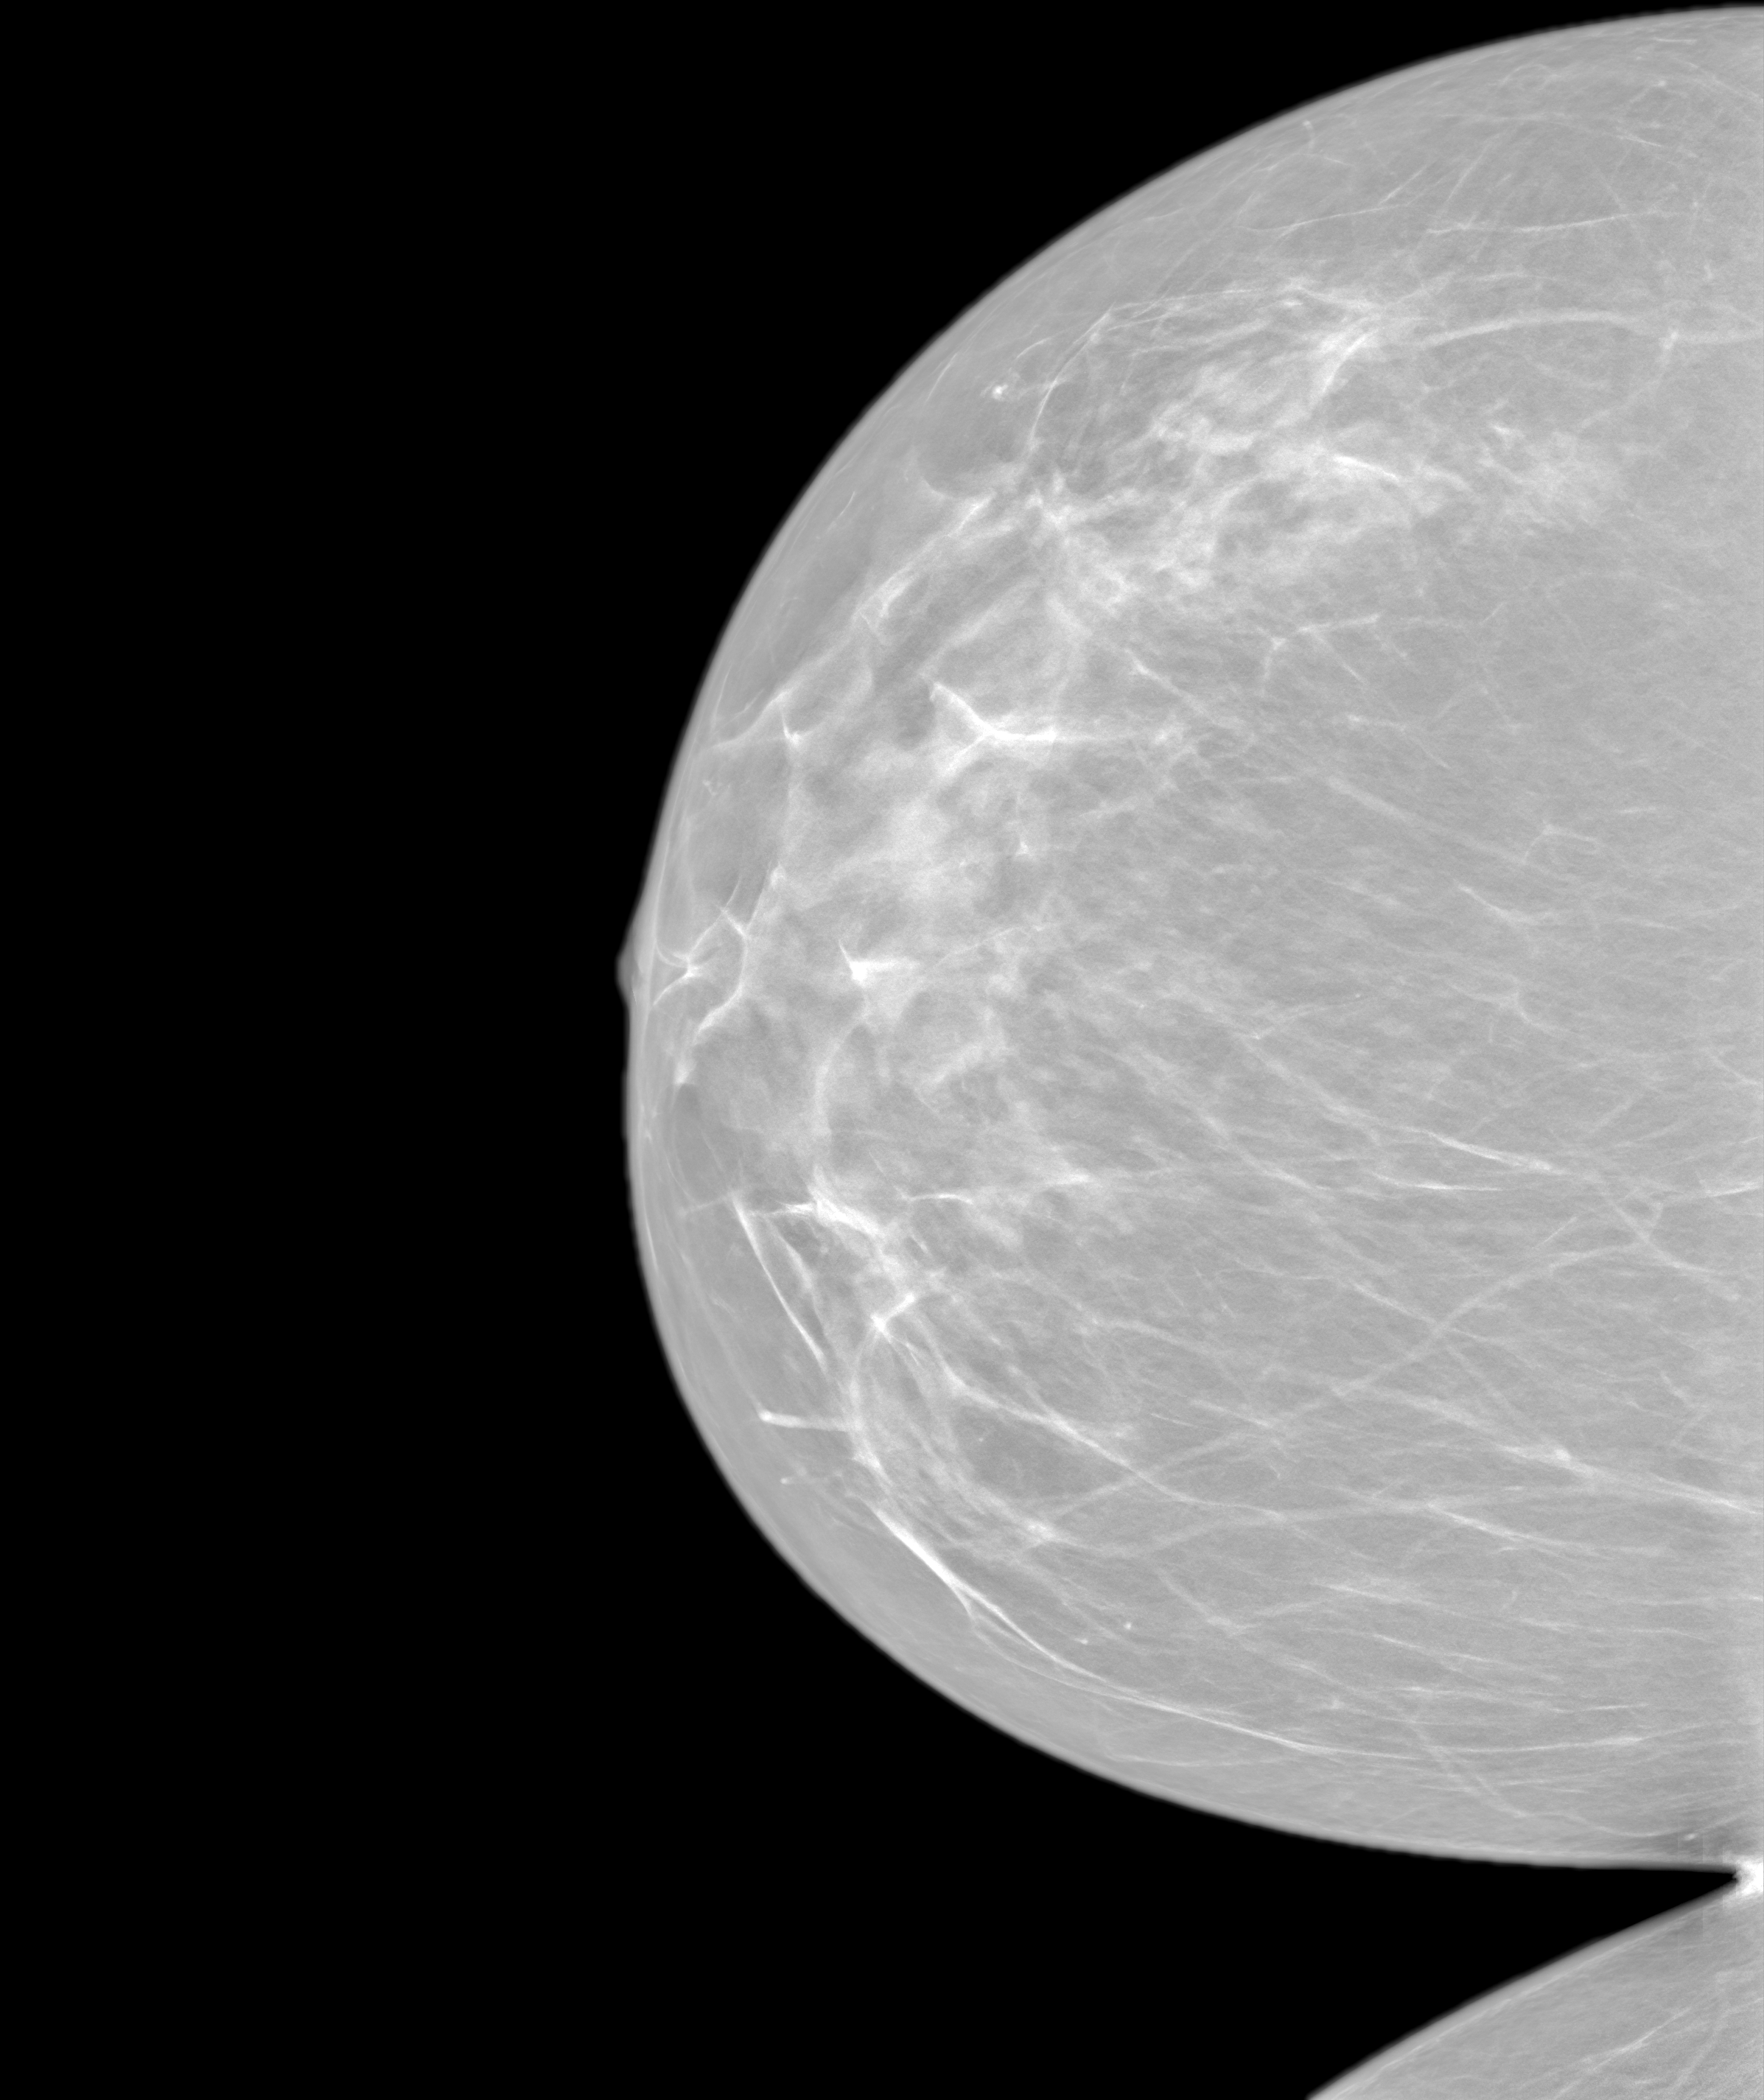
Annual screening mammography examination; system: SenoIris_1SP2(440). Female patient, age 57 years.
Image type: synthesized 2-D view from tomosynthesis. Breast: right. Projection: craniocaudal (CC) view.